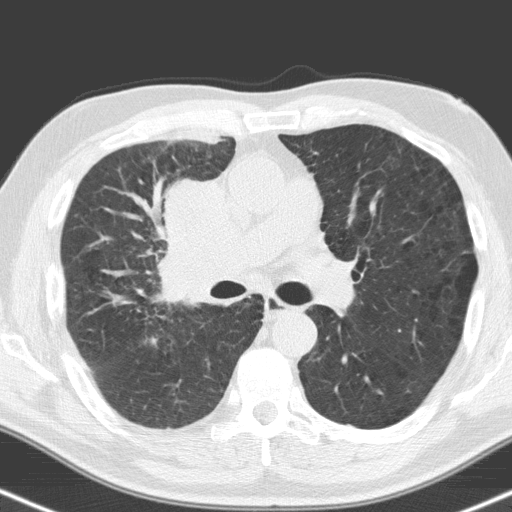
Low-dose screening chest CT, one axial slice. Position 98 of 160 along the scan axis. Lung window (W 1500 / L -600 HU). 3.2 mm slice thickness. 512 × 512 image matrix, field of view 324 × 324 mm.
Annotated regions visible in this slice (expert manual segmentation):
- lesion 1 (tumor, hilum of right lung): bounding box [x1, y1, x2, y2] px = [159, 180, 249, 302]